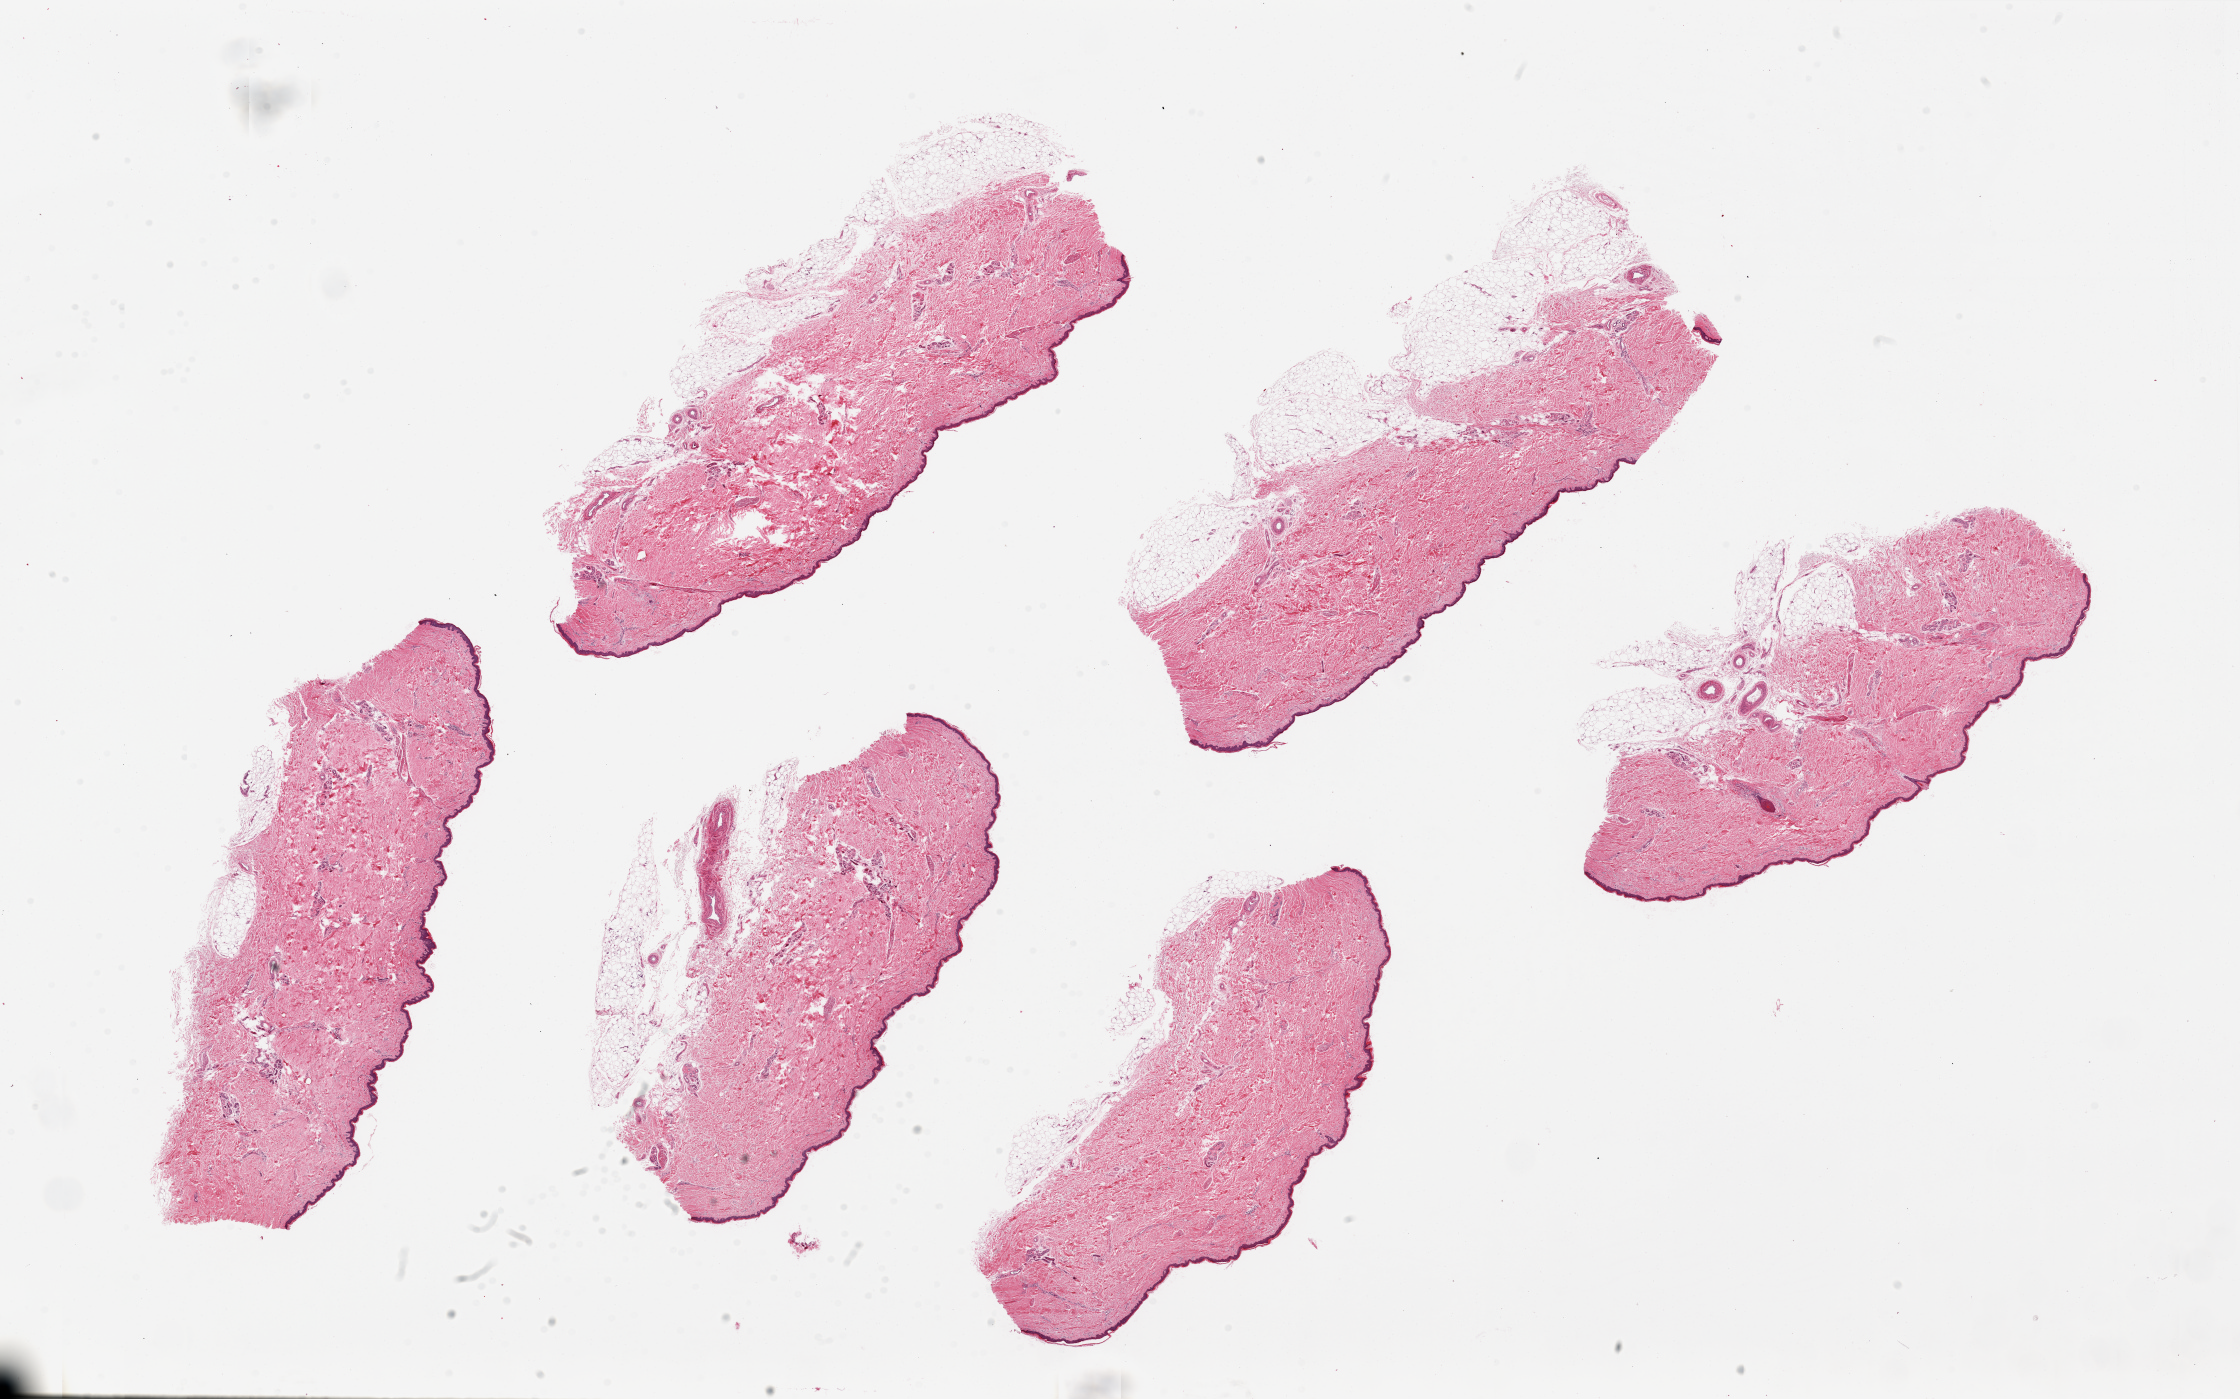
Digitized haematoxylin and eosin-stained section, brightfield — low-resolution overview of the scanned area, about 35.4 x 22.1 mm (acquisition: 20x scan), PAXgene-fixed, paraffin-embedded tissue, sampled site (target tissue): skin of lower leg, donor tissue sample. Donor: male.
Review note (as recorded): 6 pieces, up to 10x4mm; squamous epithelium is ~2% thickness. Adherent subcutaneous fat on several, up to 1.5mm thick.